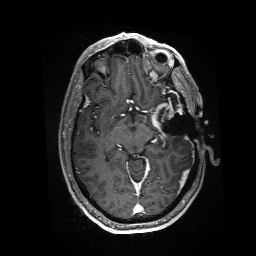
Brain MRI from a brain-tumour surgery series, one axial slice; slice 95 of 176 in the series (ordered by position); T1-weighted post-contrast; 1 mm slice thickness; 256 × 256 image matrix, field of view 256 × 256 mm. Case-level facts recorded for this patient, not image findings: histopathology: Glioblastoma; WHO grade: 4; IDH mutation: no; tumour location: Left Anterior/Superior Temporal.
Annotated regions visible in this slice (outlined manually by an expert reader):
- residual tumour: bounding box <151,102,184,132> (left, top, right, bottom; pixels)